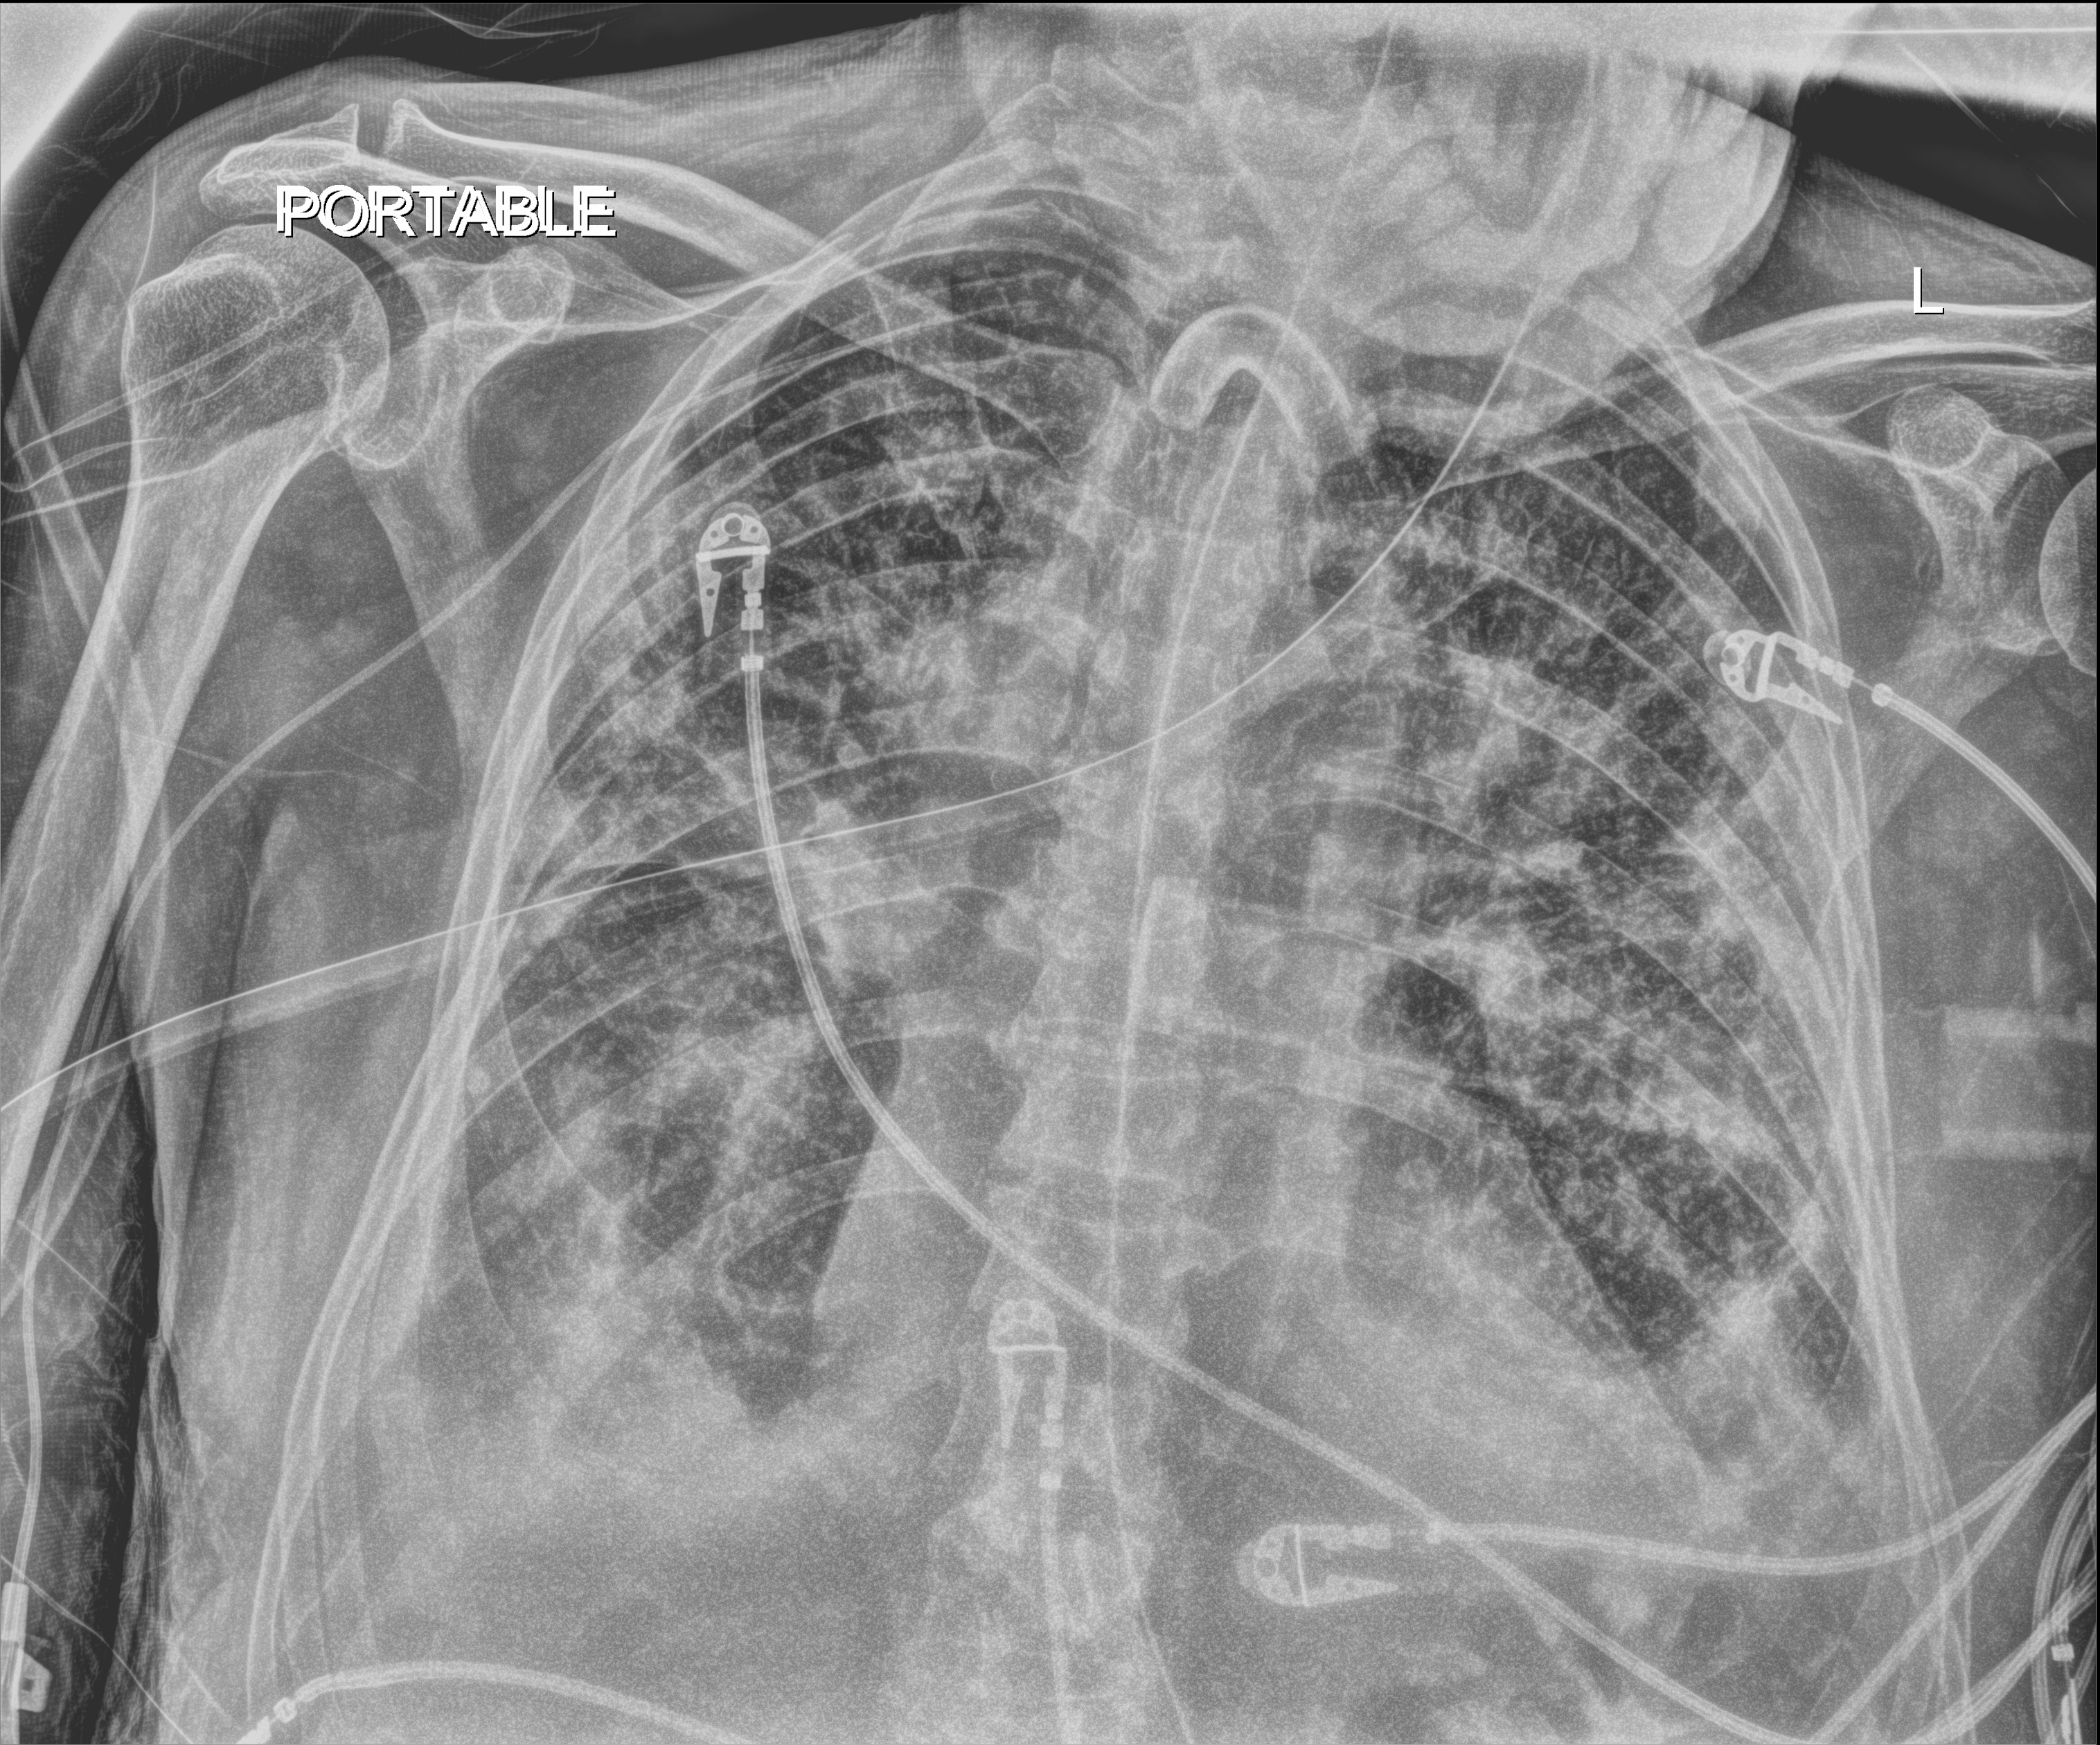
Chest X-ray (portable). Patient hospitalised with COVID-19; male, aged 75–90 years.
From the hospital-stay record, not from the radiograph (when in the stay this image was taken is not recorded):
- length of hospital stay: 70 days
- COPD (admission record): no